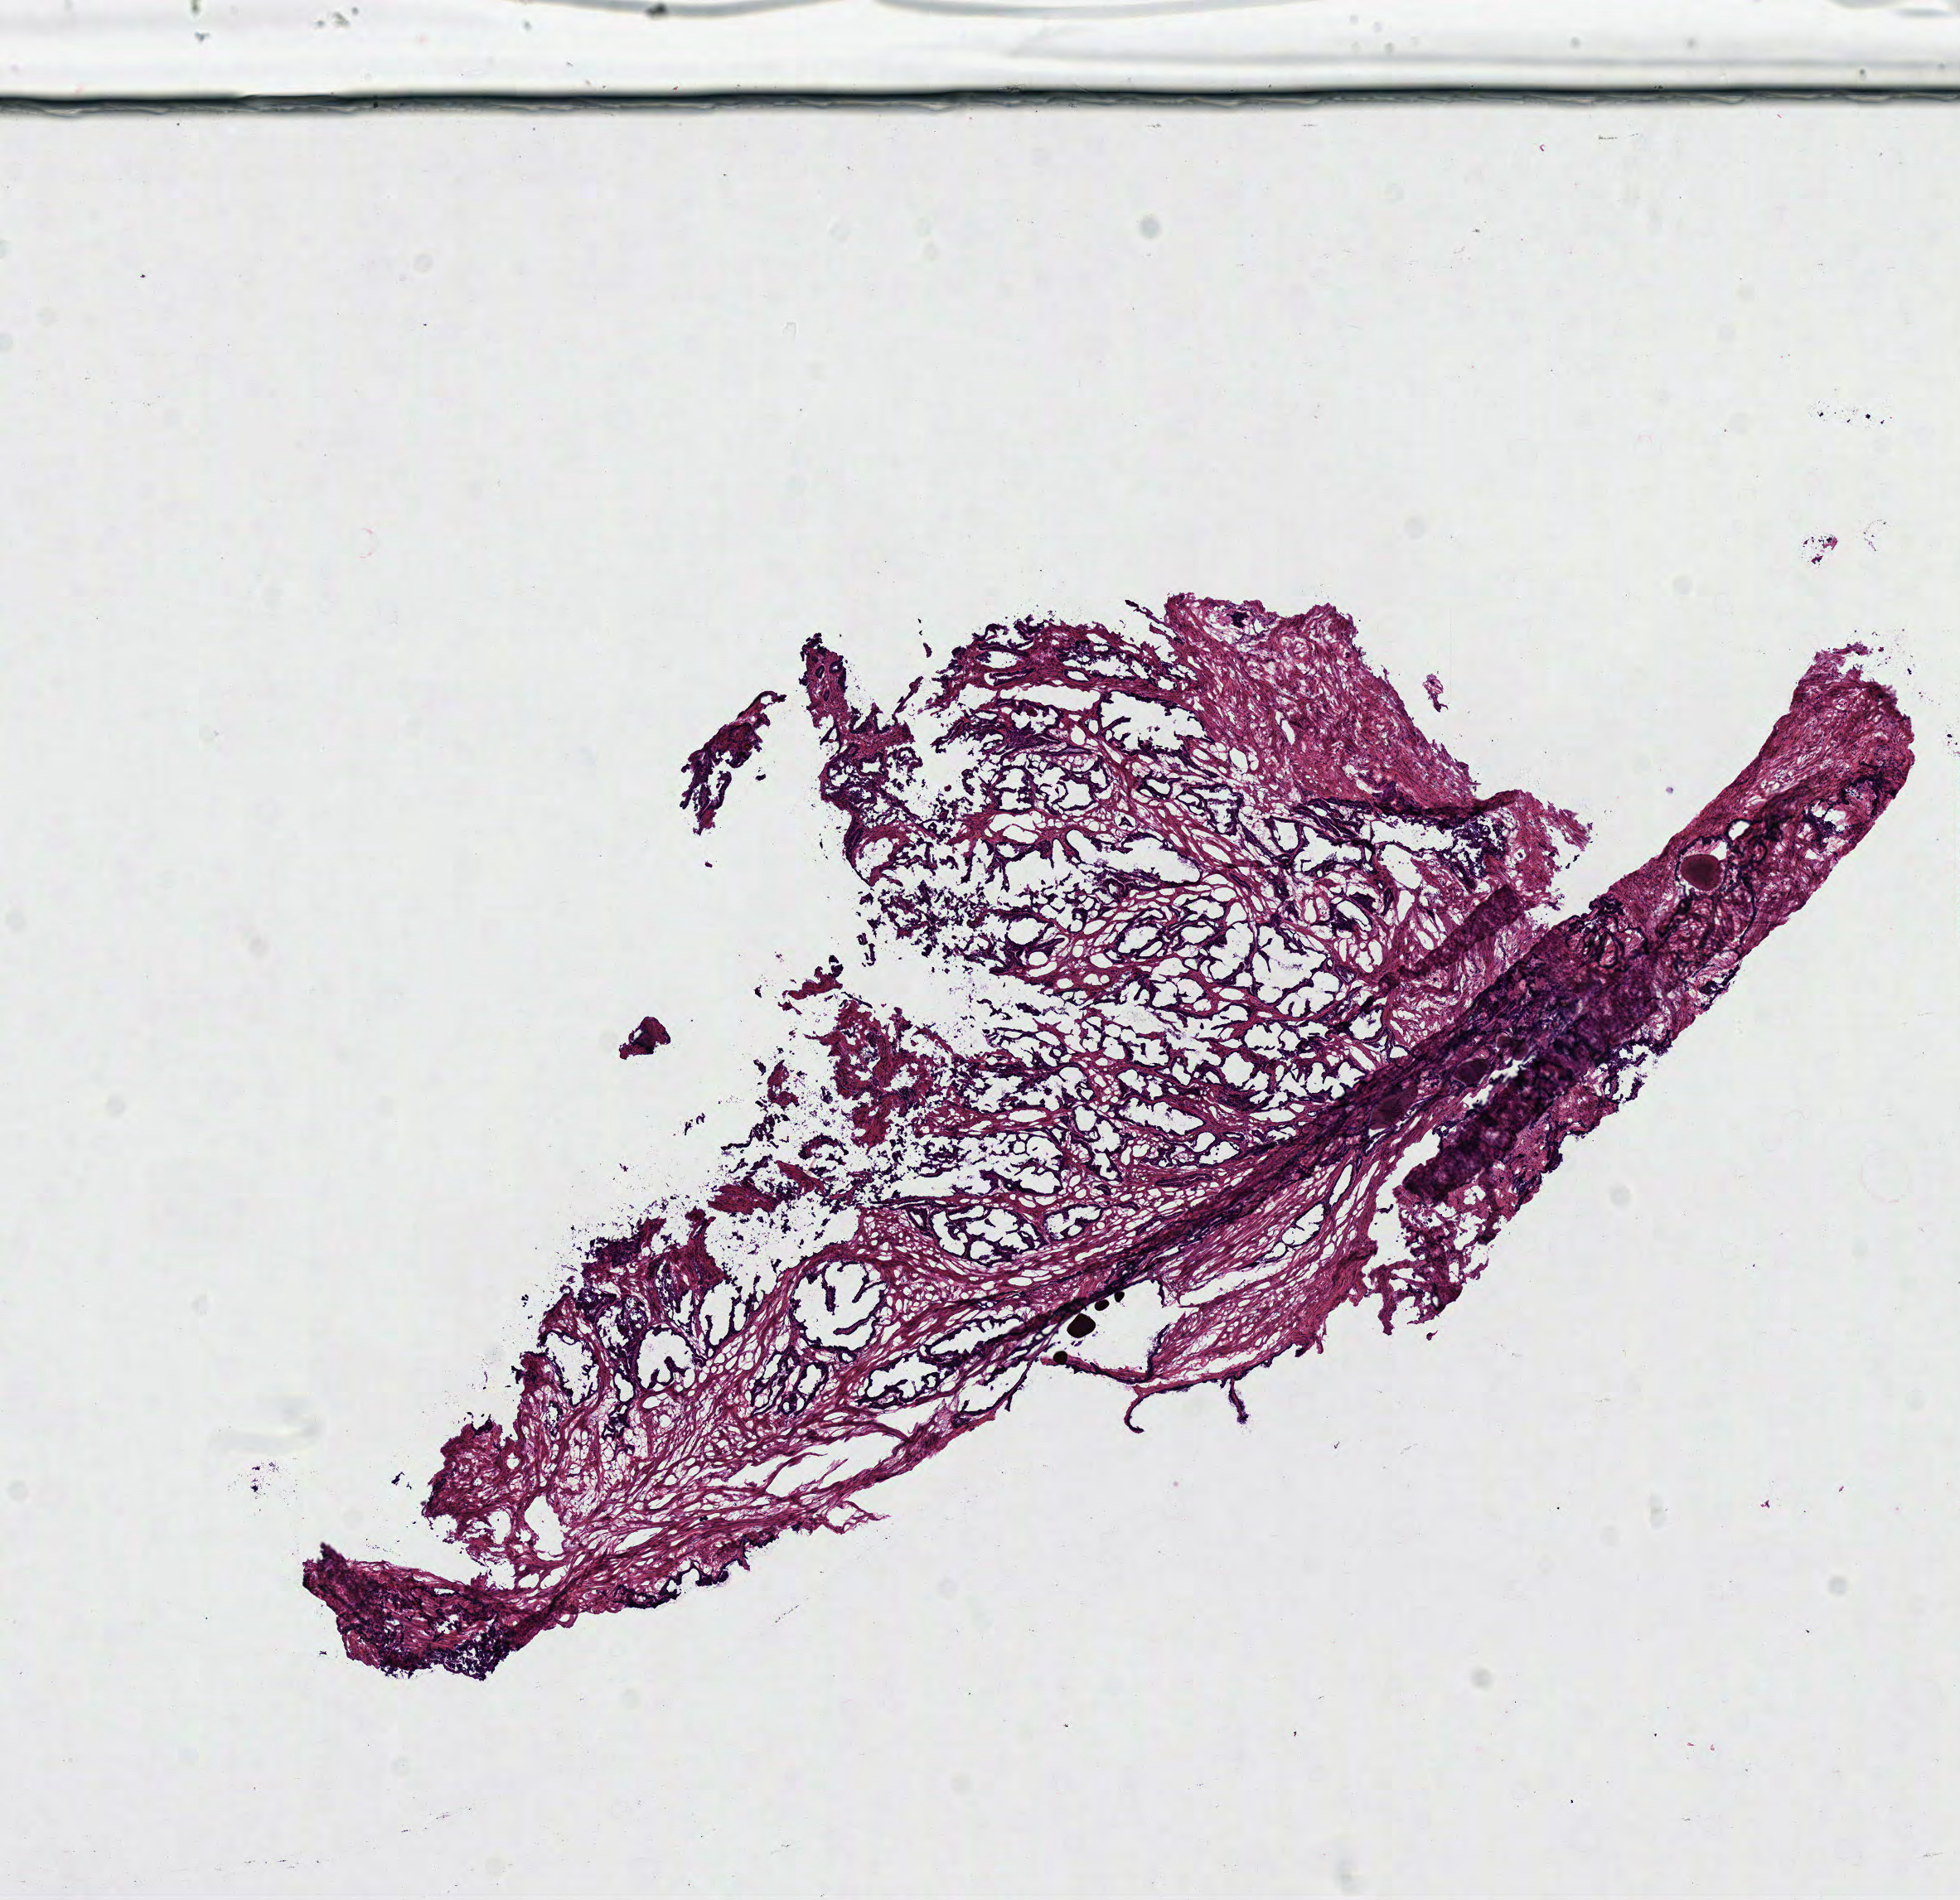
Hematoxylin and eosin (H&E) stained whole-slide image, whole scanned area (about 9.3 x 9.0 mm) shown as a low-resolution overview. Frozen section from the top of the tissue portion. Solid tissue normal (non-tumour tissue) sample from the prostate. Patient: male, age at initial diagnosis 66 years.
This section: solid tissue normal sample (biorepository sample class). Patient diagnosis: Acinar cell carcinoma.